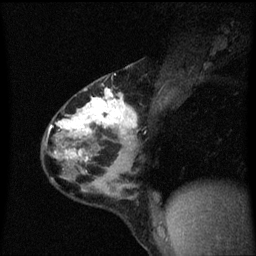
Breast MRI (dynamic contrast-enhanced), one sagittal slice; position 37 of 60 along the scan axis; dynamic contrast-enhanced series, image 2 of 3 at this slice position (ordered by acquisition); 1.5 T; TE 4.2 ms, TR 8.4 ms; 2 mm slice thickness; 256 × 256 image matrix, field of view 200 × 200 mm. Patient: female, 32 years.
Structures marked on this image (semi-automatically segmented with operator editing):
- analysis volume of interest (the breast-tissue region the enhancement analysis was run in; not a lesion): box from (x=42, y=74) to (x=140, y=169) px
- tumour enhancement mask (voxels above the 70 % enhancement threshold inside the analysis volume of interest): (x=51, y=88)–(x=138, y=163)